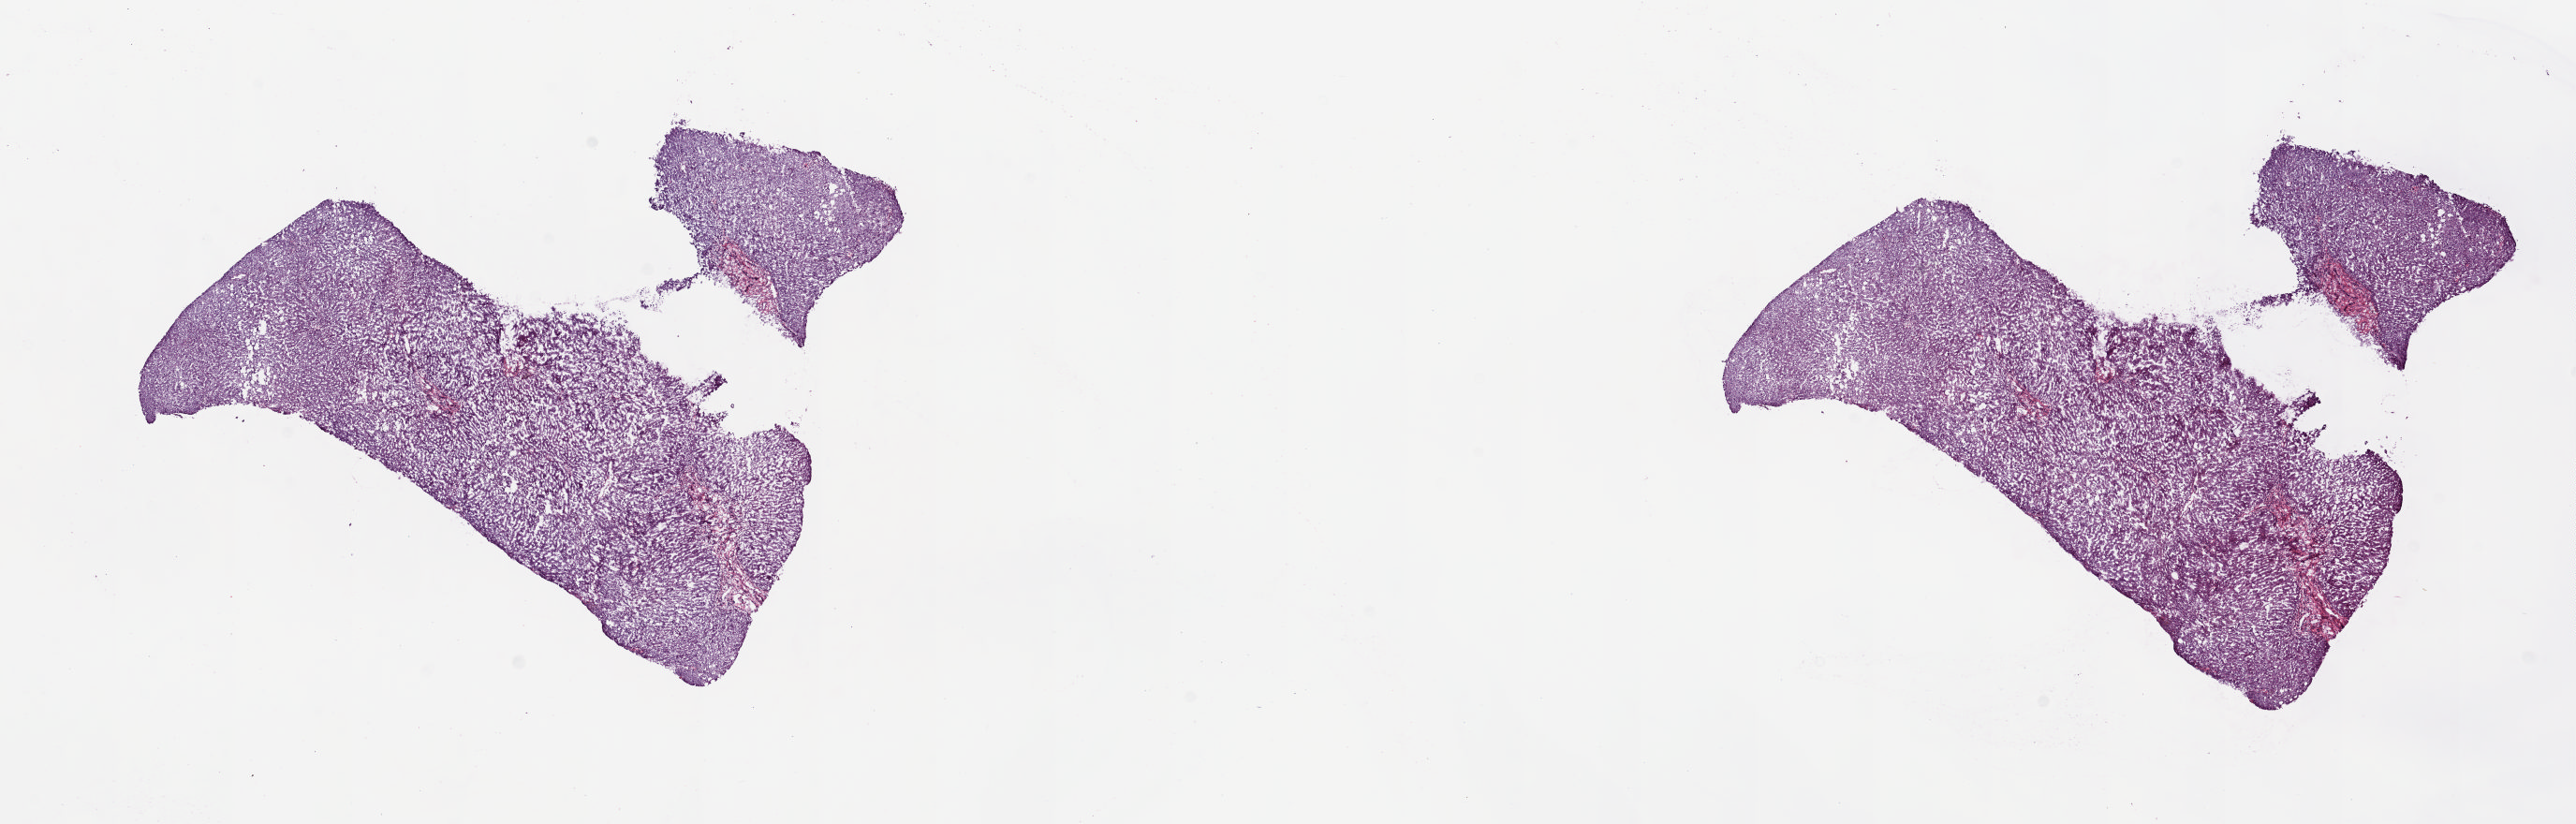
H&E whole-slide image, shown as a low-resolution overview of the whole scanned area (about 21.8 x 7.0 mm), frozen section from the top of the tissue portion, sample: solid tissue normal (non-tumour tissue), bile duct. Male, age 52 years at initial diagnosis. Composition of this section per pathologist review: tumour cells 0%, tumour nuclei 0%, normal cells 100%, stromal cells 0%, necrosis 0%. Inflammatory infiltration, as recorded: lymphocyte infiltration 0%, monocyte infiltration 0%, neutrophil infiltration 0%.
• this section: solid tissue normal (non-tumour) sample from the same patient
• patient diagnosis: Cholangiocarcinoma